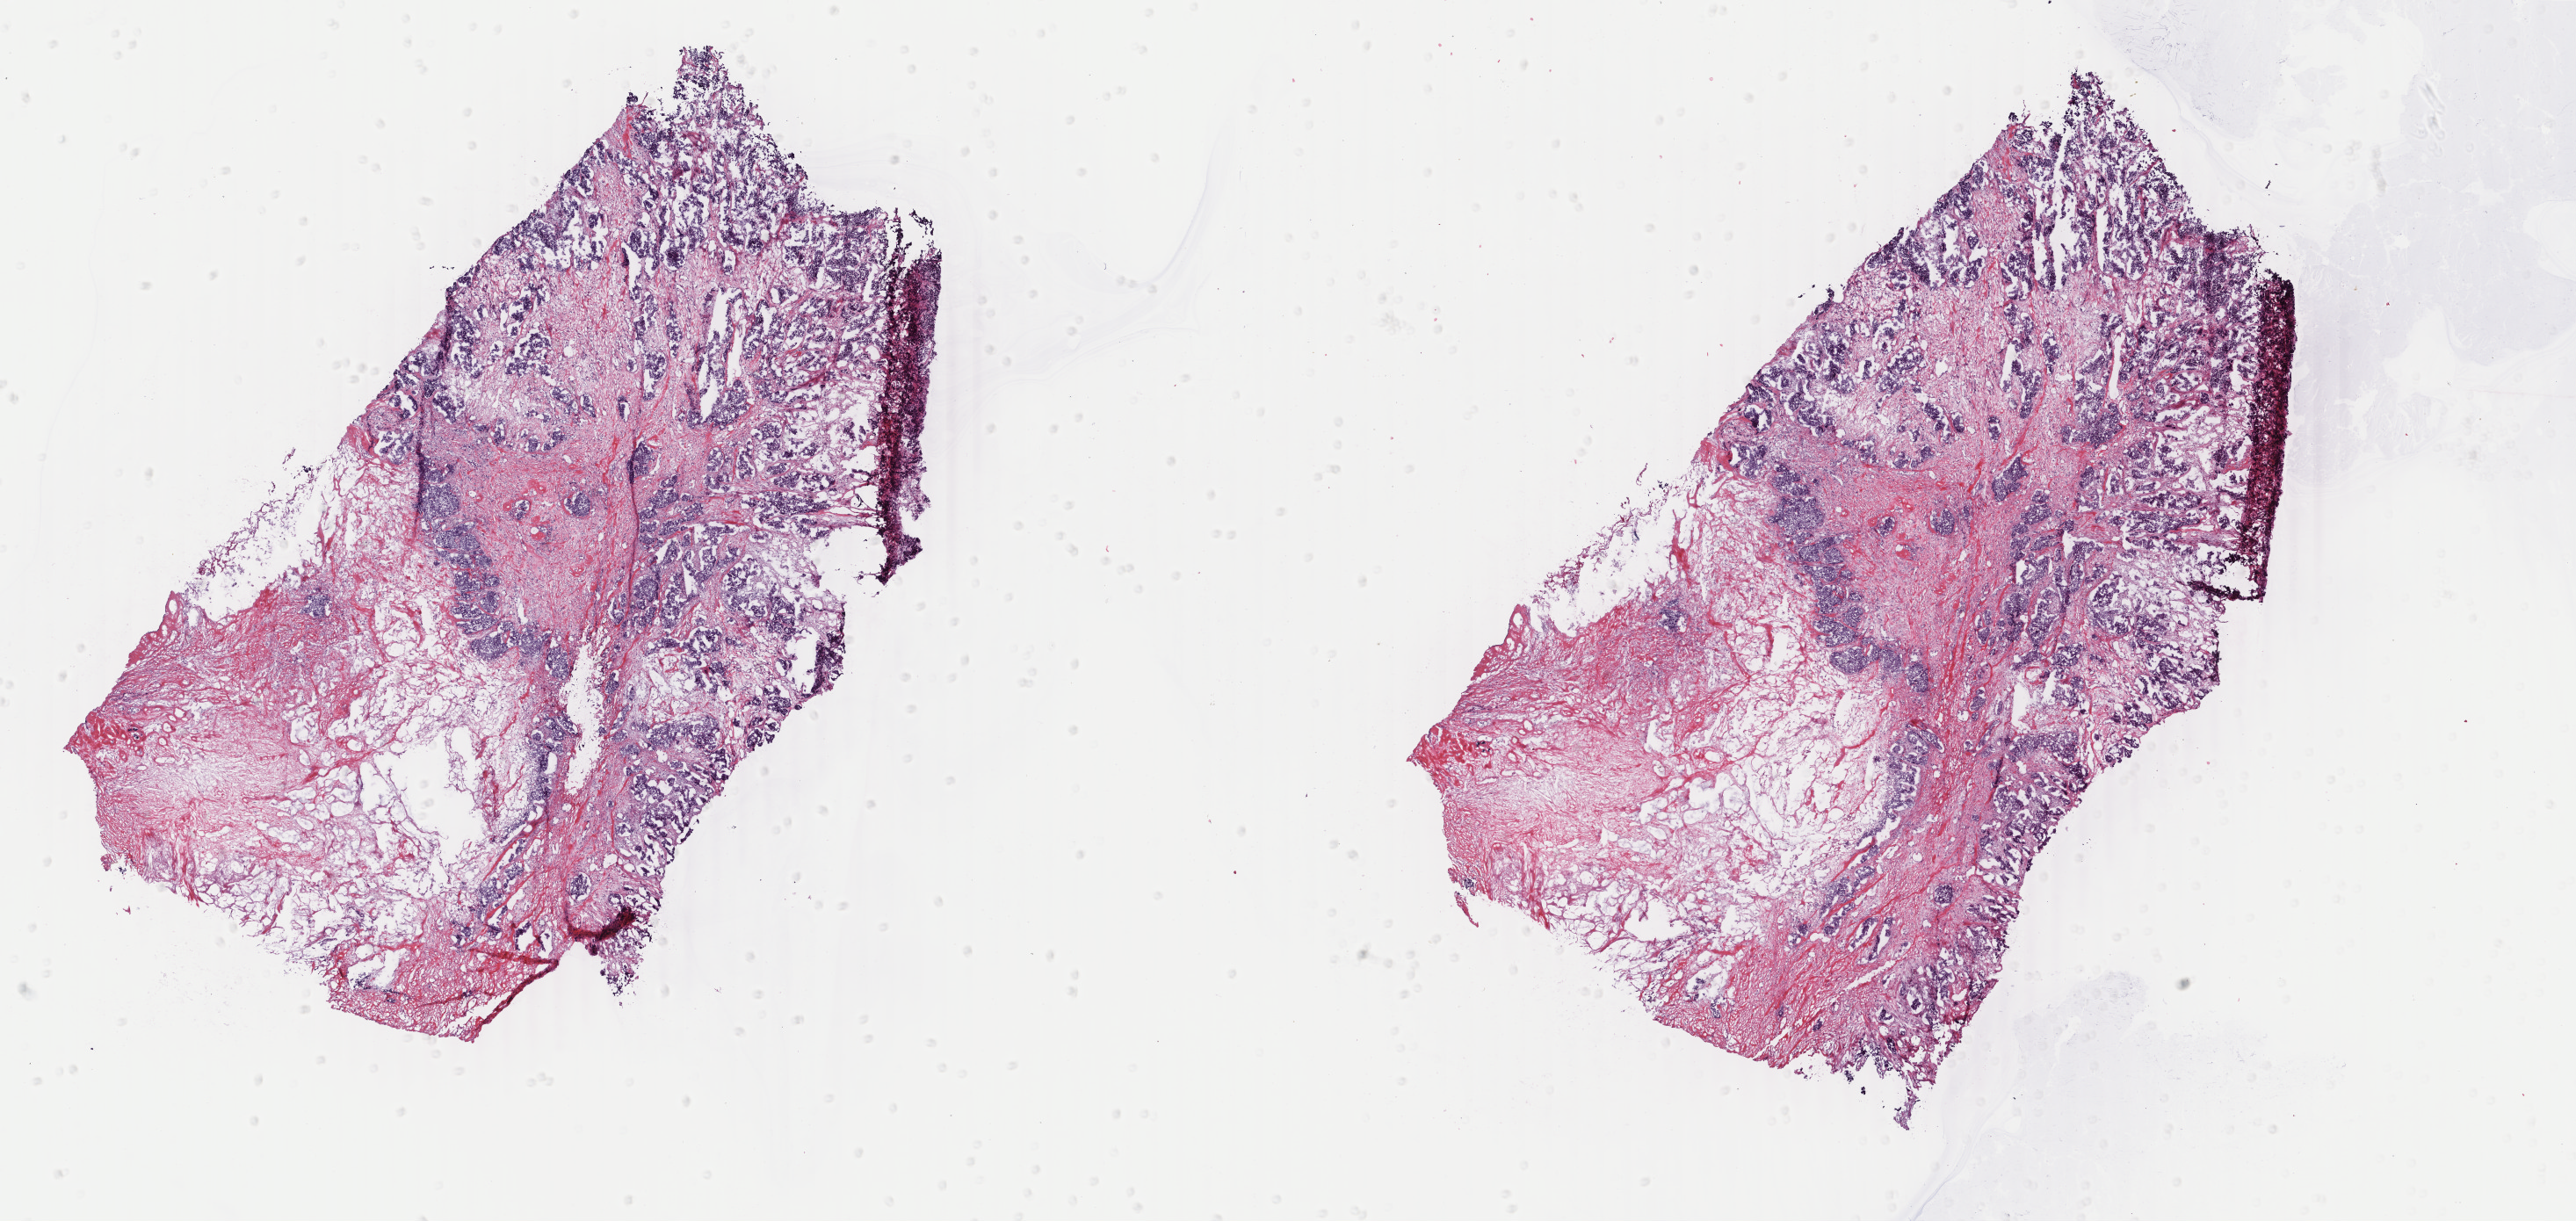
Digitized H&E tissue section (whole slide), whole scanned area (about 23.3 x 11.1 mm) shown as a low-resolution overview. Frozen section. Primary tumour sample from the breast. Female, age 63 years at initial diagnosis. Slide review estimates, as recorded: tumour cells 60%, tumour nuclei 80%, normal cells 0%, stromal cells 40%, necrosis 0%. Infiltration values recorded for this section: lymphocyte infiltration 0%, monocyte infiltration 0%, neutrophil infiltration 0%.
Laterality: left. Lymph nodes positive (case pathology): 1 of 22 examined. Diagnosis: Infiltrating duct carcinoma, NOS. AJCC pathologic stage: IIB.